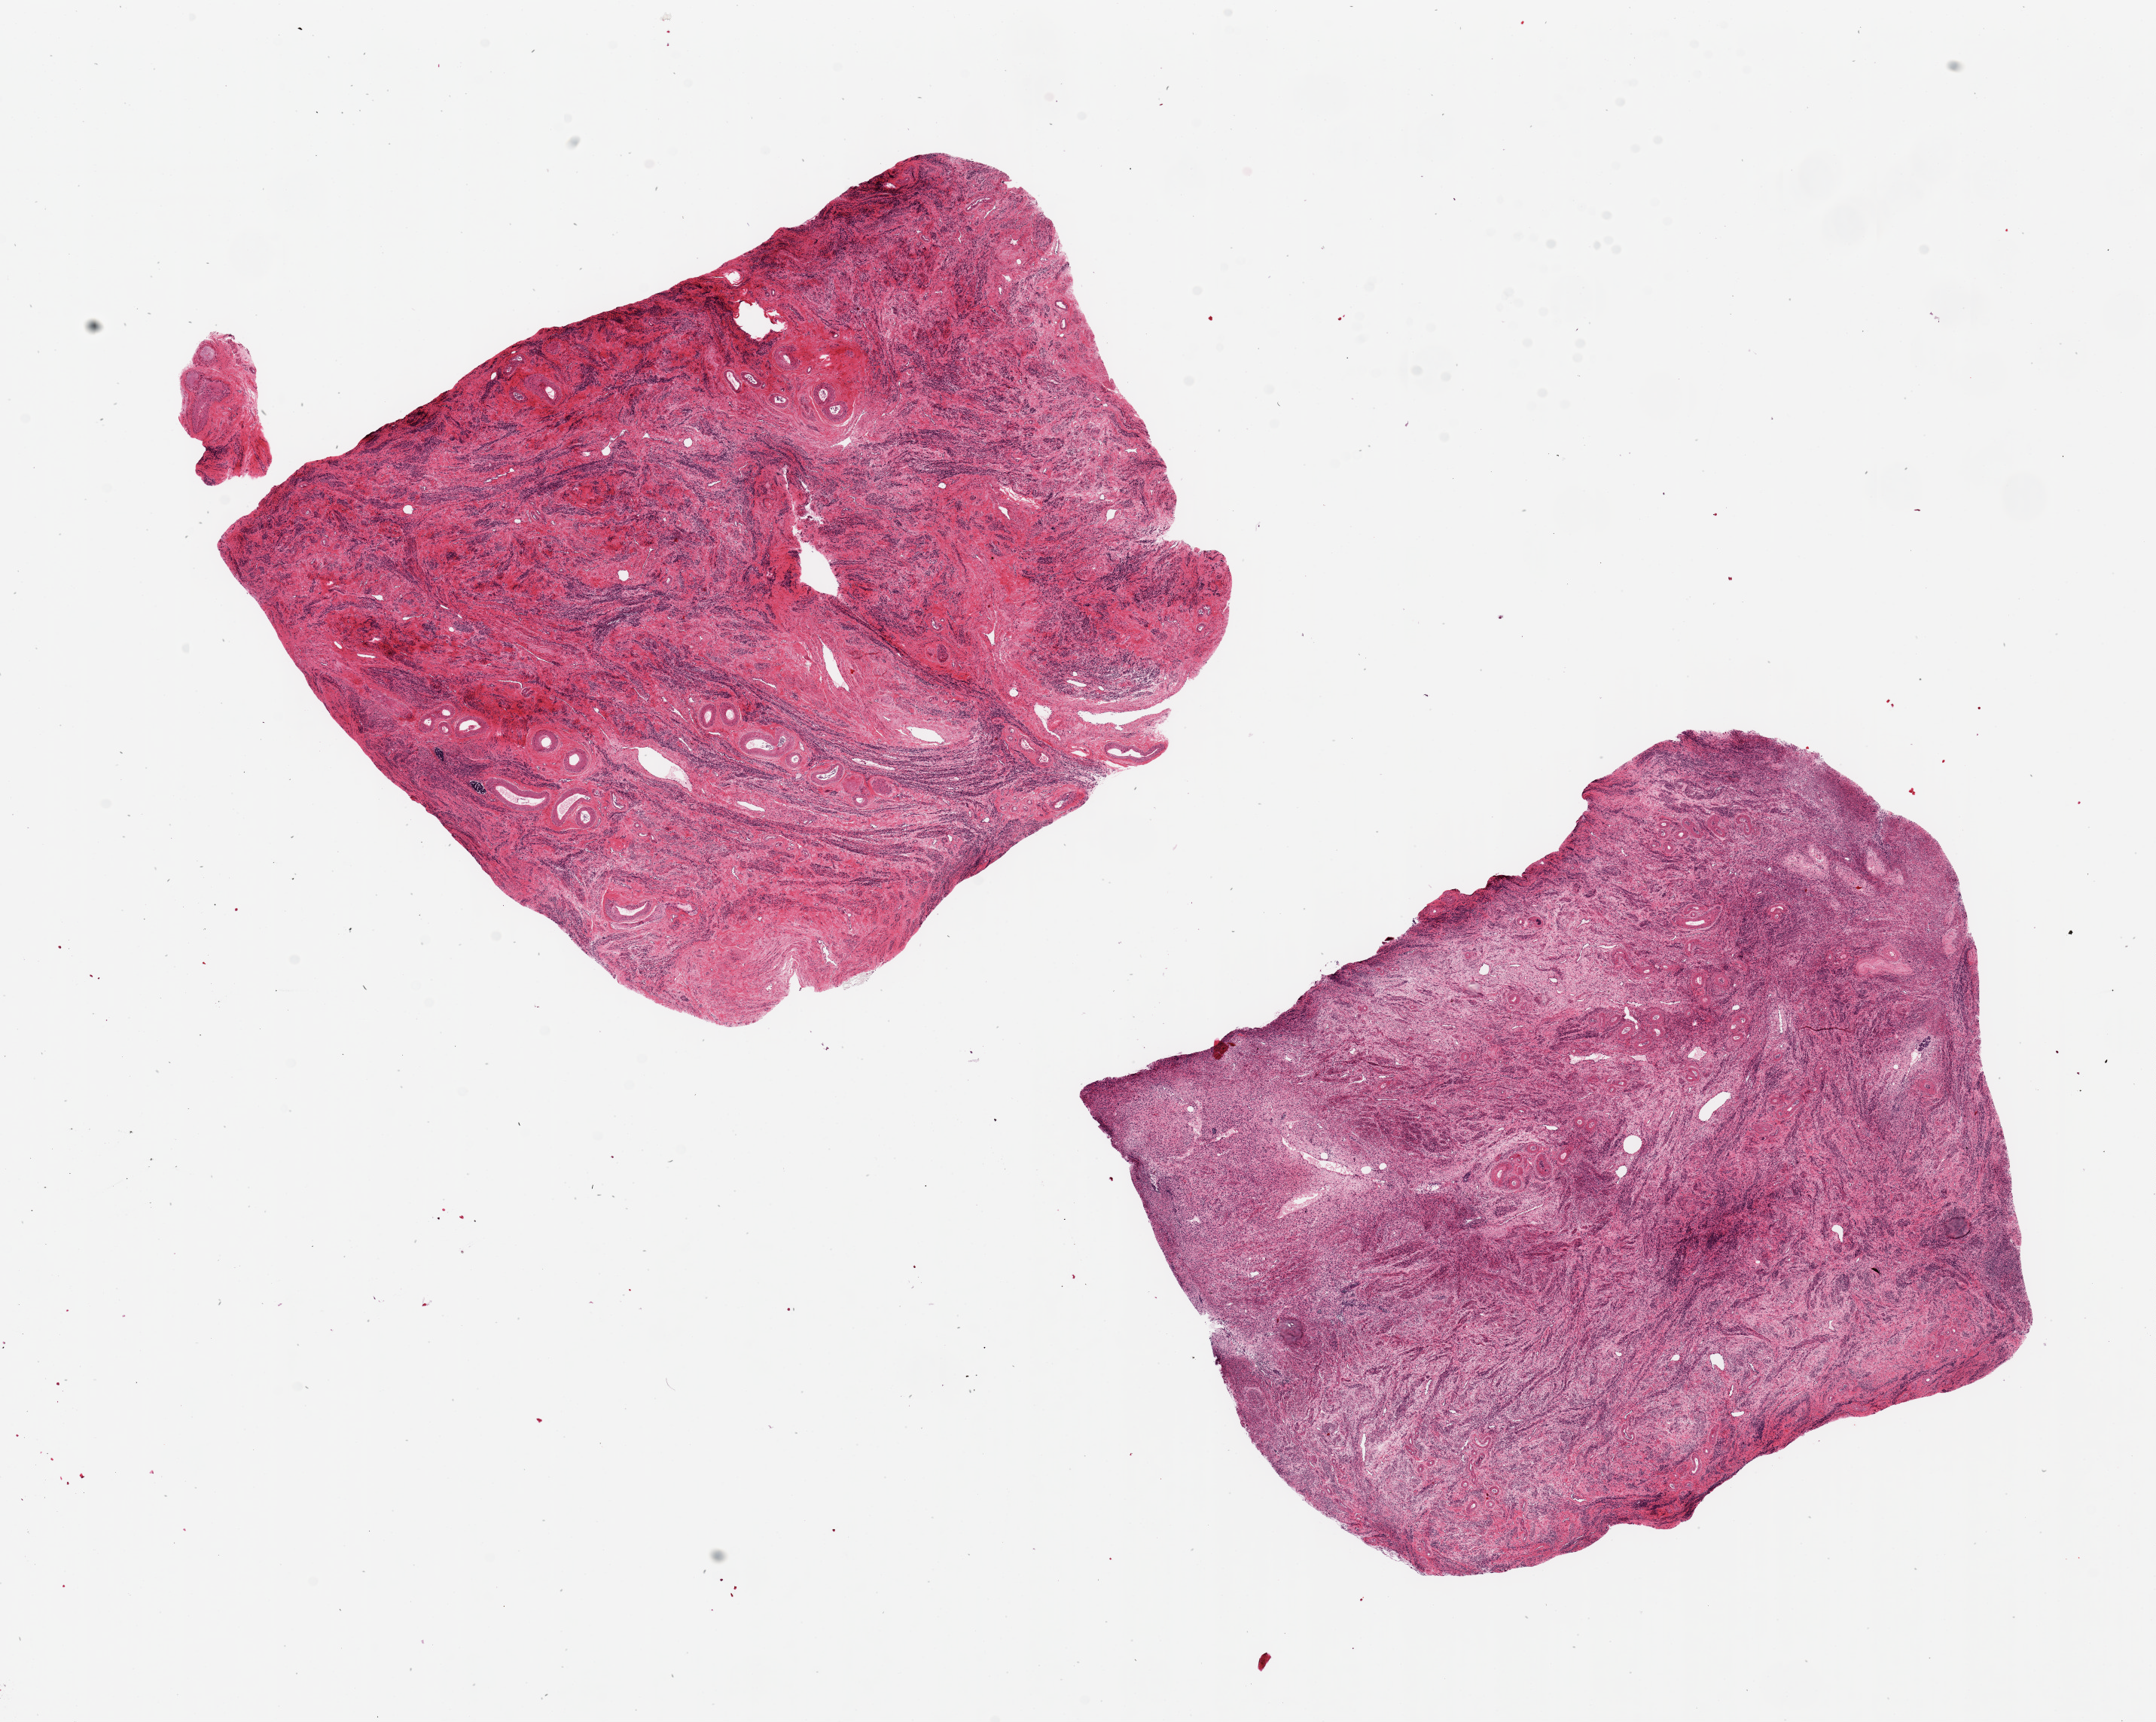
Whole-slide image, haematoxylin and eosin stain — low-resolution overview of the scanned area, about 22.6 x 18.1 mm. PAXgene-fixed, paraffin-embedded tissue. Section of uterus (target tissue). Tissue donor sample. Female donor.
* pathologist's review note for this sample: 2 pieces, 9x7 & 8x7mm; no endometrium visible